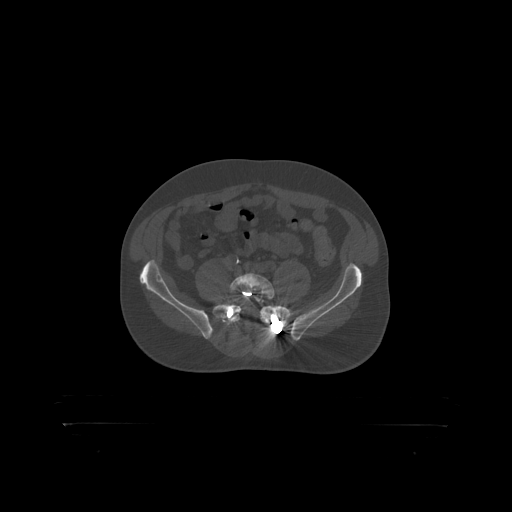
CT including the spine, one axial slice; position 194 of 399 along the scan axis; 120 kVp; bone window (W 1800 / L 400 HU); 1.25 mm slice thickness; 512 × 512 image matrix, field of view 650 × 650 mm. Male patient, age 46 years. From the clinical record (not read from this slice): primary cancer: skin.
Structures marked on this image (semi-automatically segmented with operator editing):
- L5 vertebra: box from (x=230, y=274) to (x=275, y=300) px